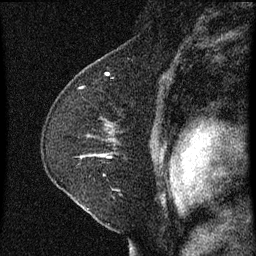
Breast MRI (dynamic contrast-enhanced), one sagittal slice; slice 45 of 60 in the series (ordered by position); dynamic contrast-enhanced series, image 2 of 3 at this slice position (ordered by acquisition); 1.5 T; TE 4.2 ms, TR 8 ms; 2 mm slice thickness; 256 × 256 image matrix. Female patient, age 47 years.
Annotated regions visible in this slice (semi-automatic segmentation, software-assisted and operator-edited):
- analysis volume of interest (the breast-tissue region the enhancement analysis was run in; not a lesion): bounding box (x1, y1, x2, y2) in pixels: (43, 98, 158, 213)
- tumour enhancement mask (voxels above the 70 % enhancement threshold inside the analysis volume of interest): (101, 154, 106, 157)